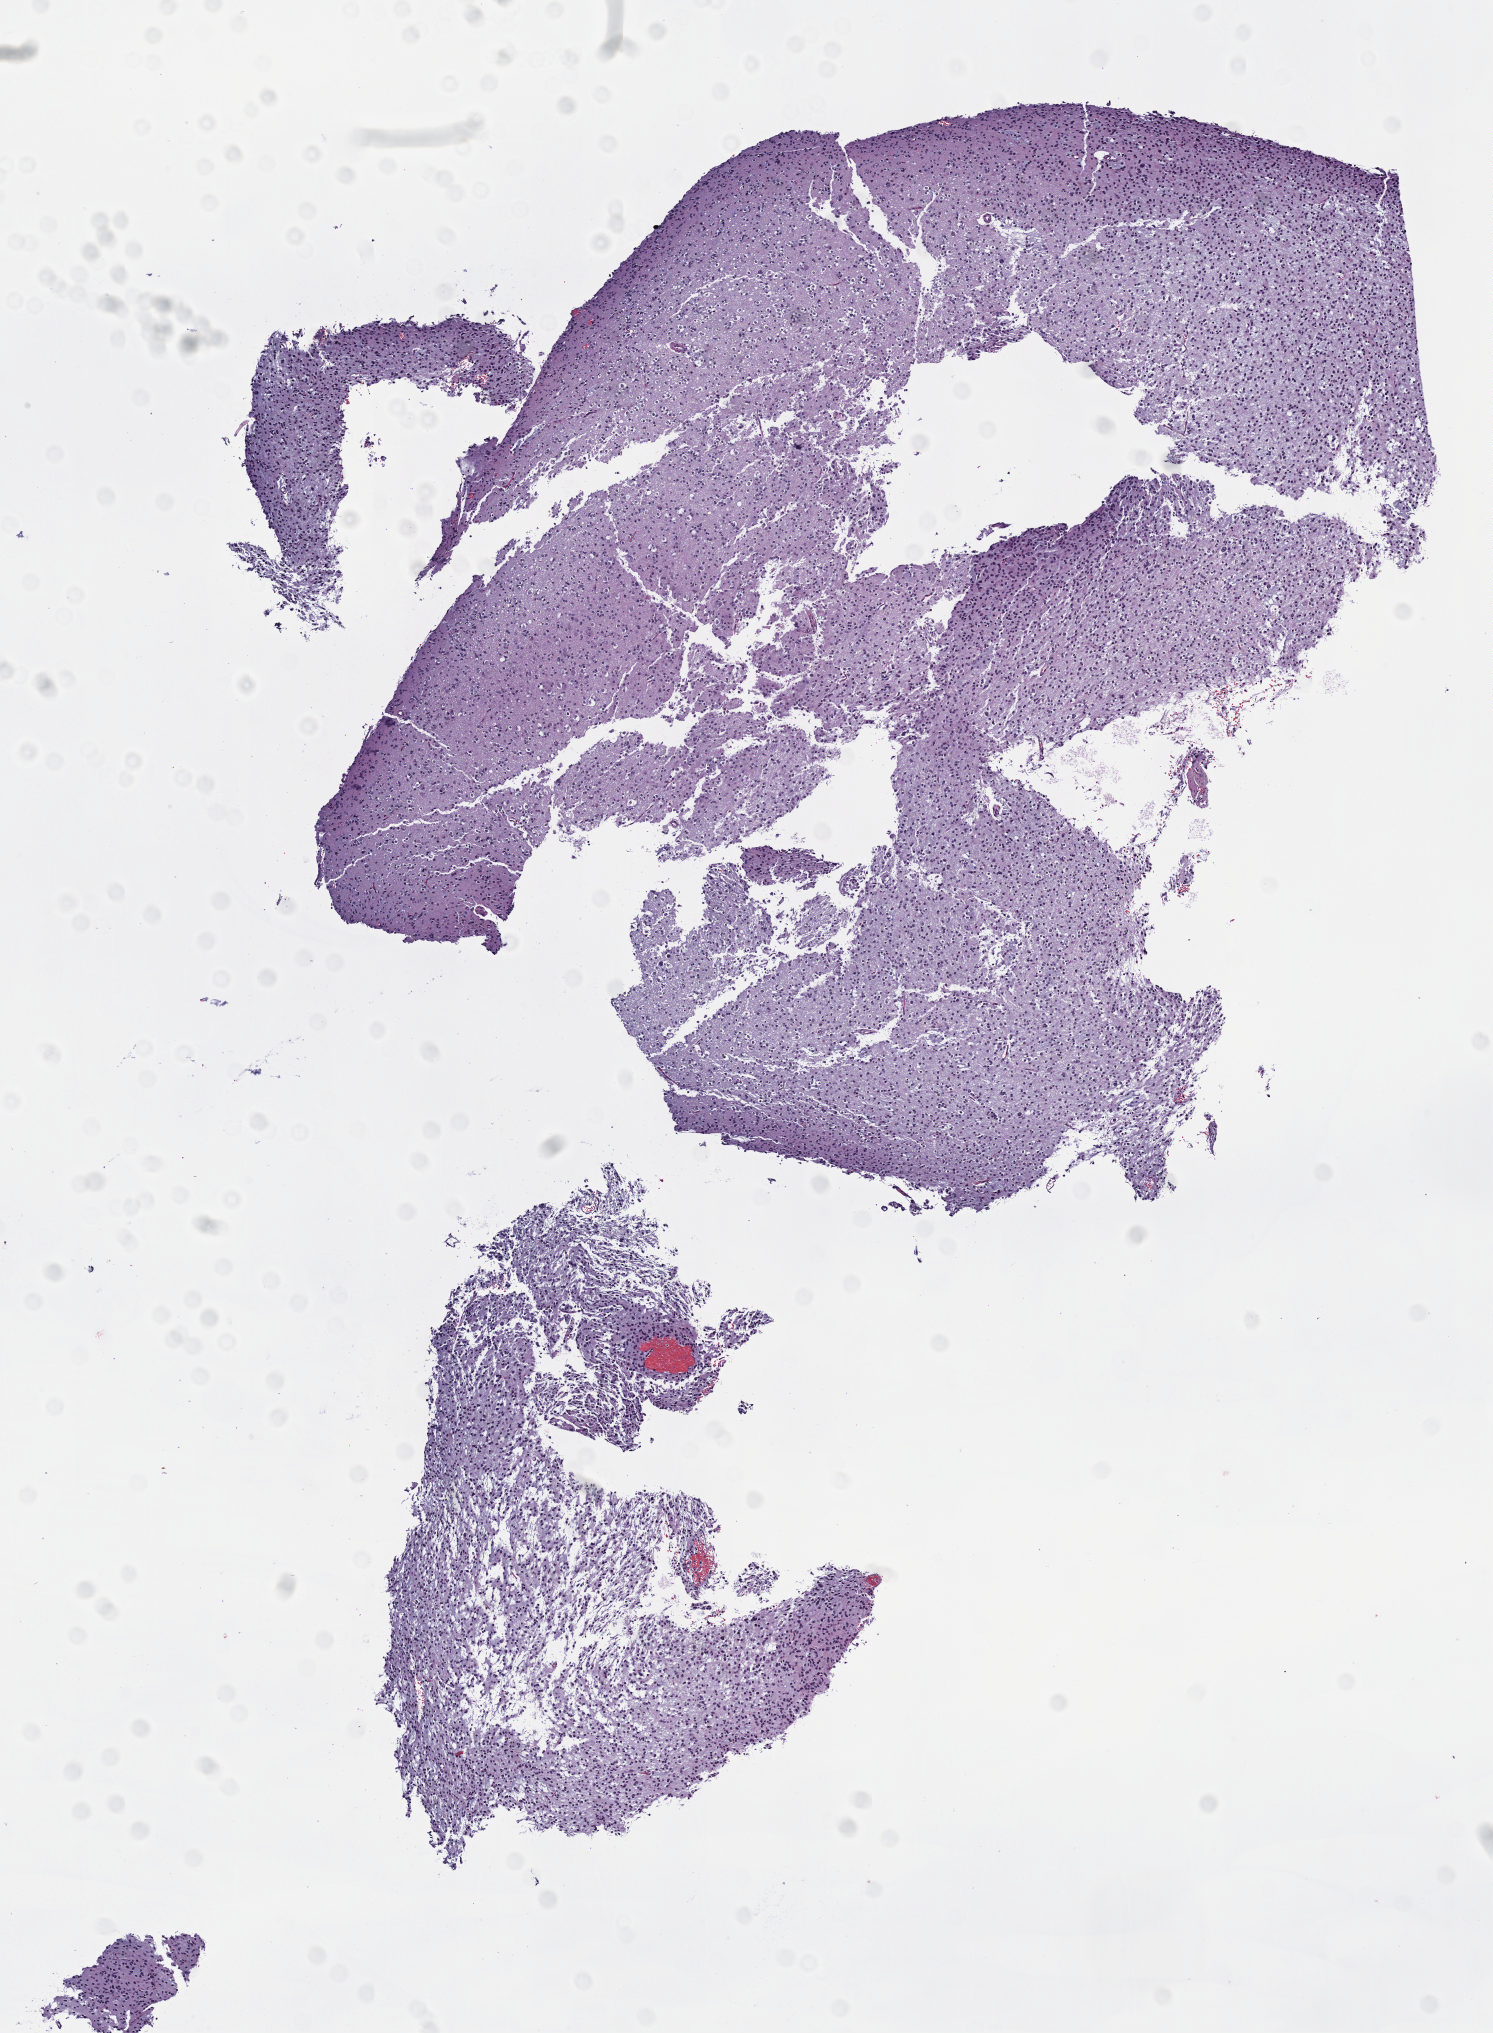
Whole-slide histology image, H&E, low-resolution overview of the scanned area, about 6.0 x 8.2 mm. Formalin-fixed paraffin-embedded (FFPE) diagnostic section. Primary tumour sample from the brain. Patient: female, age at initial diagnosis 50 years. Histologic grade: G2 (moderately differentiated).
Pathologic diagnosis: Oligodendroglioma, NOS (cerebrum).